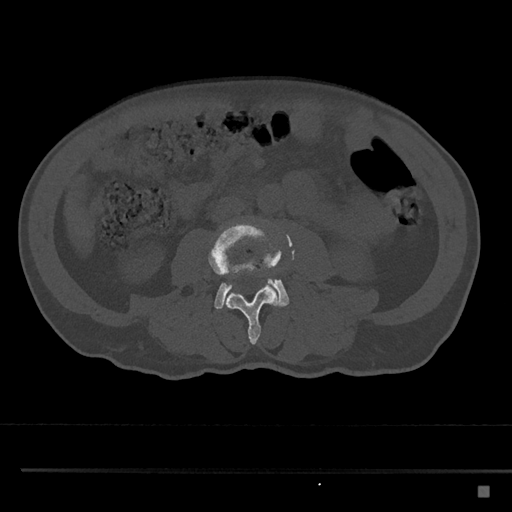
CT including the spine, one axial slice; position 672 of 797 along the scan axis; reconstruction kernel Br40s/3; bone window (W 1800 / L 400 HU); 0.5 mm slice thickness; 512 × 512 image matrix, field of view 391 × 391 mm. Male patient, age 59 years. Case-level facts recorded for this patient, not image findings: primary cancer: prostate.
Structures marked on this image (semi-automatically segmented with operator editing):
- L3 vertebra: bounding box [x1, y1, x2, y2] px = [208, 221, 281, 345]
- L4 vertebra: [214, 266, 290, 309]